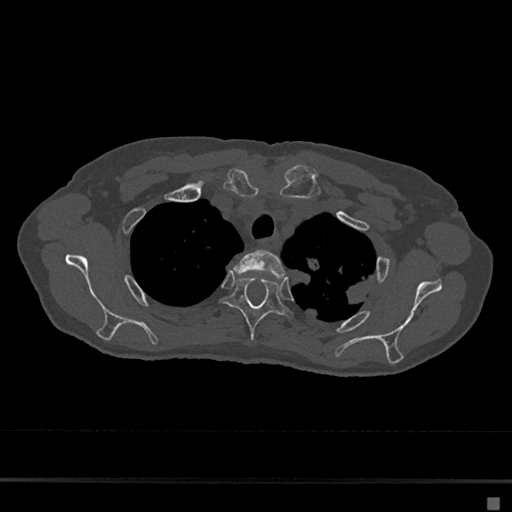
CT including the spine, one axial slice; slice 546 of 797 in the series (ordered by position); reconstruction kernel Br40s/3; 120 kVp; bone window (W 1800 / L 400 HU); 0.5 mm slice thickness; 512 × 512 image matrix, field of view 360 × 360 mm. Patient: female, 68 years. Case-level facts recorded for this patient, not image findings: primary cancer: renal.
Annotated regions visible in this slice (semi-automatically segmented with operator editing):
- T2 vertebra: bounding box (x1, y1, x2, y2) in pixels: (232, 250, 285, 279)
- T3 vertebra: (220, 277, 293, 343)